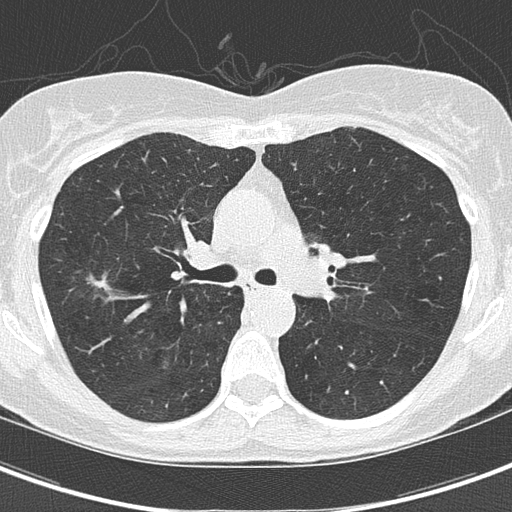
Axial slice from a low-dose chest CT screening exam. Third annual screen. Lung window (W 1500 / L -600 HU). 2 mm slice thickness. Slice 56 of 154 in the series. Female participant, aged 59 years at enrolment. Current smoker at enrolment.
Expert-annotated lung lesion, bounding box [x1, y1, x2, y2] px = [70, 261, 128, 314]. Reader record for this screening exam (exam-level; its link to the box is not recorded): non-calcified nodule or mass ≥4 mm, right upper lobe, 10 × 8 mm, poorly defined margins, ground glass attenuation, pre-existing on the prior screen: yes; interval growth: yes. Official screen result: positive, other. Later outcome: lung cancer diagnosed 63 days after this screen — bronchiolo-alveolar adenocarcinoma, NOS, right upper lobe, well differentiated (G1), stage IA (AJCC 6th edition), 4 mm at pathology.